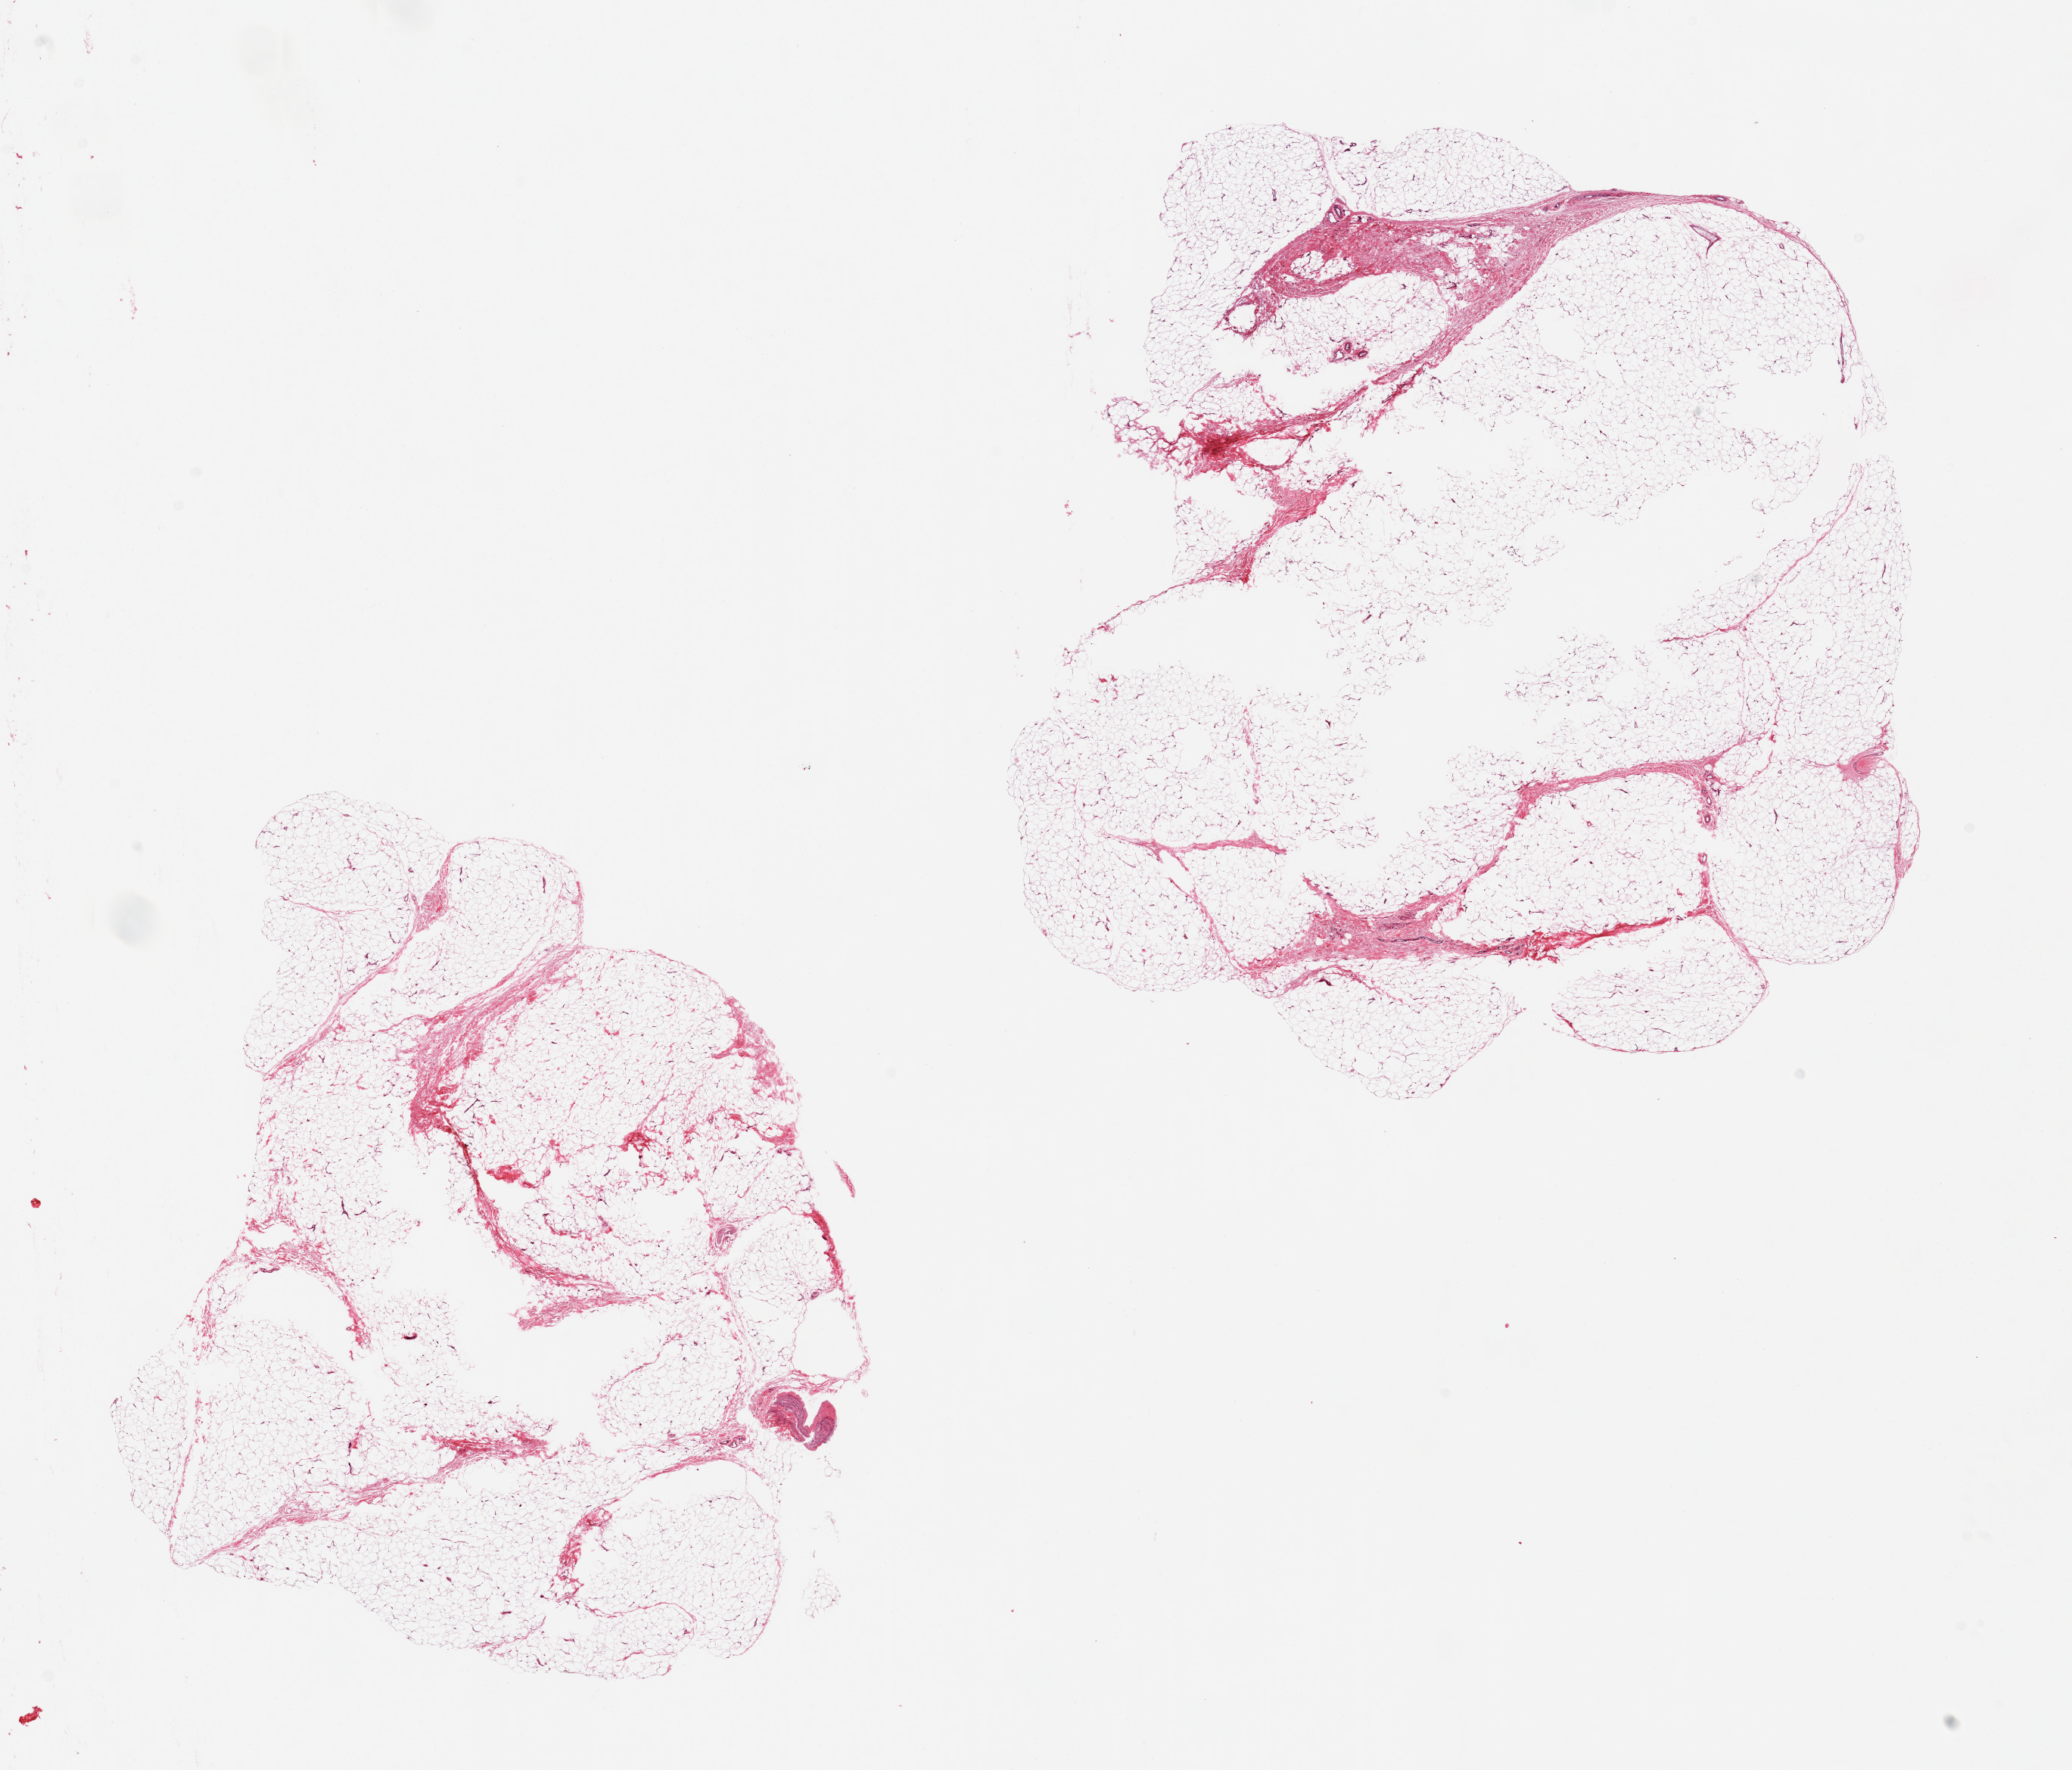
Hematoxylin and eosin (H&E) whole-slide image — shown as a low-resolution overview of the whole scanned area (about 21.7 x 18.5 mm); PAXgene-fixed paraffin-embedded (PFPE) section; section of adipose tissue (target tissue); donor tissue sample. Donor sex: female.
Review note (as recorded): 2 pieces, ~10% fibro-fascial tissue.